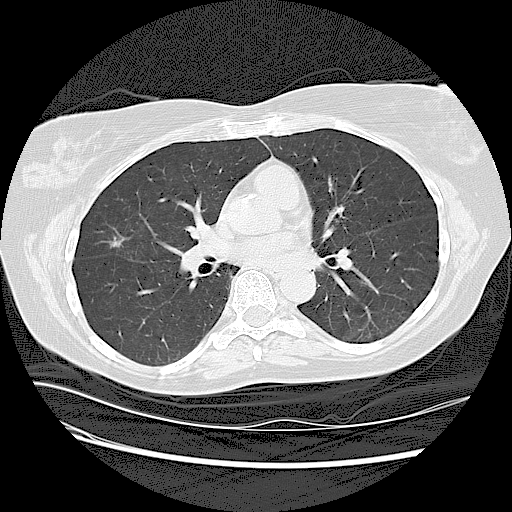
Low-dose screening chest CT, one axial slice. Position 62 of 125 along the scan axis. Lung window (W 1500 / L -600 HU). 2.5 mm slice thickness. 512 × 512 image matrix, field of view 360 × 360 mm.
Outlined on this slice (expert manual segmentation):
- lesion 1 (tumor, upper lobe of right lung): bounding box (x1, y1, x2, y2) in pixels: (107, 228, 127, 247)